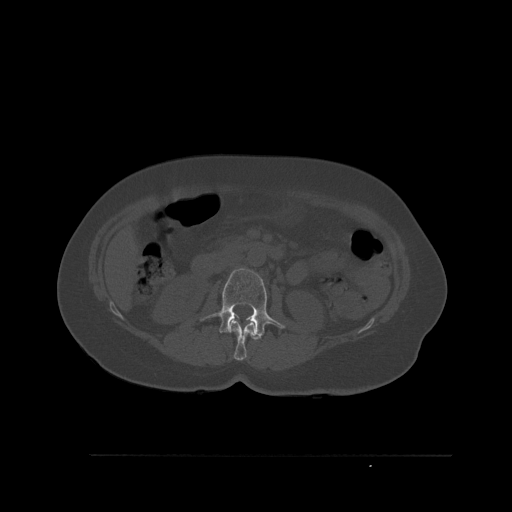
CT including the spine, one axial slice. Position 251 of 527 along the scan axis. Bone window (W 1800 / L 400 HU). 1.5 mm slice thickness. 512 × 512 image matrix. Female patient, age 73 years. Case-level facts recorded for this patient, not image findings: primary cancer: breast; vertebrae with lytic lesions (as recorded): L2.
Structures marked on this image (semi-automatically segmented with operator editing):
- L1 vertebra: bounding box [x1, y1, x2, y2] px = [229, 318, 260, 361]
- L2 vertebra: [200, 268, 285, 338]